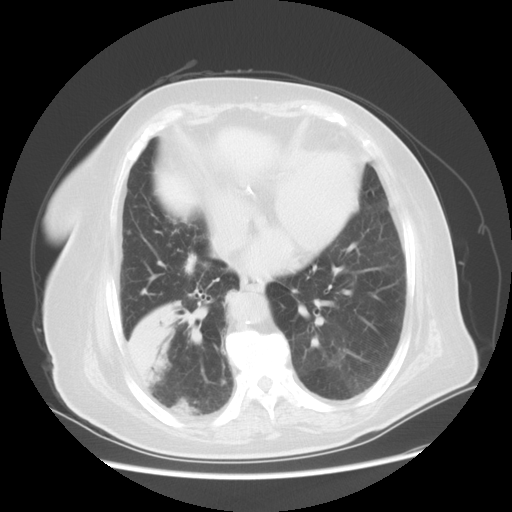
Chest CT, one axial slice. Slice 21 of 56 in the series (ordered by position). Reconstruction kernel STANDARD. 120 kVp. Lung window (W 1500 / L -600 HU). 512 × 512 image matrix, field of view 378 × 378 mm. Patient: female, 73 years. From the clinical record (not read from this slice): clinical TNM (as recorded): T3 N0 M0.
Outlined on this slice (rectangle marked by the reading radiologist):
- lung tumour (recorded histology: adenocarcinoma): bounding box [x1, y1, x2, y2] px = [123, 300, 186, 389]